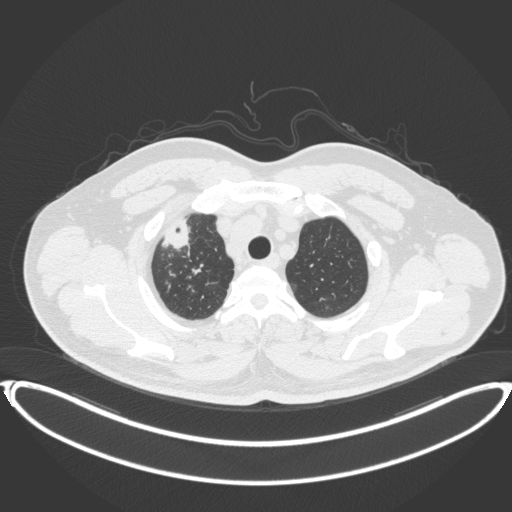
Chest CT, one axial slice; position 335 of 399 along the scan axis; reconstruction kernel B31f; lung window (W 1500 / L -600 HU); 1 mm slice thickness; 512 × 512 image matrix, field of view 445 × 445 mm. Patient: male, 53 years. From the clinical record (not read from this slice): clinical TNM (as recorded): T2a N0 M0.
Annotated regions visible in this slice (bounding box drawn by a radiologist):
- lung tumour (recorded histology: adenocarcinoma): bounding box <162,213,201,257> (left, top, right, bottom; pixels)